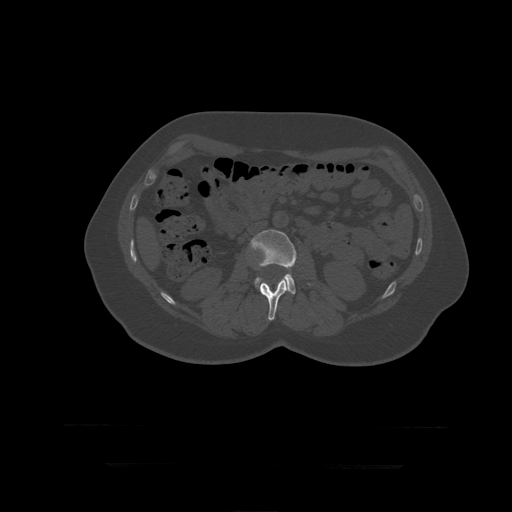
CT including the spine, one axial slice. Position 137 of 399 along the scan axis. Reconstruction kernel STANDARD. Bone window (W 1800 / L 400 HU). 1.25 mm slice thickness. 512 × 512 image matrix, field of view 450 × 450 mm. Patient age 41 years. From the clinical record (not read from this slice): primary cancer: breast.
Annotated regions visible in this slice (semi-automatically segmented with operator editing):
- L2 vertebra: box from (x=259, y=280) to (x=288, y=321) px
- L3 vertebra: (x=250, y=230)–(x=311, y=295)